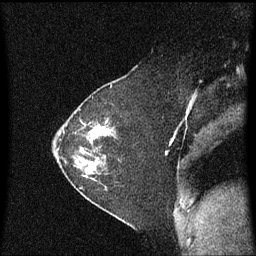
Breast MRI (dynamic contrast-enhanced), one sagittal slice. Slice 39 of 60 in the series (ordered by position). Dynamic contrast-enhanced series, image 2 of 3 at this slice position (ordered by acquisition). 1.5 T. TE 4.2 ms, TR 8.4 ms. 2 mm slice thickness. 256 × 256 image matrix. Female patient, age 36 years. Case-level facts recorded for this patient, not image findings: setting: breast cancer imaged before/during neoadjuvant chemotherapy; receptor status: HR-positive, HER2-negative.
Structures marked on this image (semi-automatically segmented with operator editing):
- analysis volume of interest (the breast-tissue region the enhancement analysis was run in; not a lesion): bounding box <66,102,121,179> (left, top, right, bottom; pixels)
- tumour enhancement mask (voxels above the 70 % enhancement threshold inside the analysis volume of interest): <88,122,112,173>